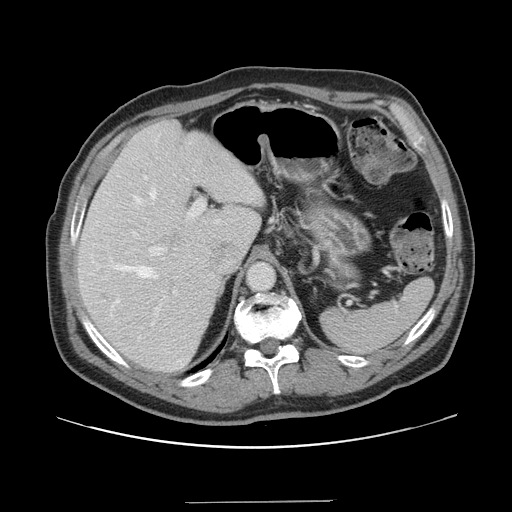
Contrast-enhanced abdominal CT, one axial slice. Position 105 of 151 along the scan axis. 120 kVp. Intravenous contrast given. Soft-tissue window (W 400 / L 40 HU). 512 × 512 image matrix, field of view 399 × 399 mm. Male patient, age 63 years. Case-level facts recorded for this patient, not image findings: diagnosis: colorectal cancer liver metastases, imaged before liver resection; multiple liver metastases: no; largest metastasis: 2.1 cm; chemotherapy before resection: no.
Outlined on this slice (expert manual segmentation):
- hepatic veins: box from (x=114, y=188) to (x=157, y=303) px
- liver: (x=78, y=120)–(x=265, y=373)
- planned liver remnant (the part of the liver to remain after resection): (x=78, y=121)–(x=261, y=373)
- portal vein (with intrahepatic branches): (x=149, y=199)–(x=205, y=316)